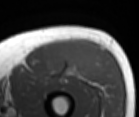
MRI of an extremity soft-tissue mass, one axial slice. Position 42 of 86 along the scan axis. MR volume resampled by the dataset authors to the PET/CT grid (not the native acquisition matrix). 3.27 mm slice thickness. 139 × 117 image matrix, field of view 136 × 114 mm. Male patient. Case-level facts recorded for this patient, not image findings: histological type: extraskeletal osteosarcoma; grade: high; site of the primary tumour: thigh.
Annotated regions visible in this slice (expert contour drawn on MRI and transferred to this co-registered scan by the dataset authors):
- gross tumour volume (mass): bounding box (x1, y1, x2, y2) in pixels: (56, 41, 98, 76)